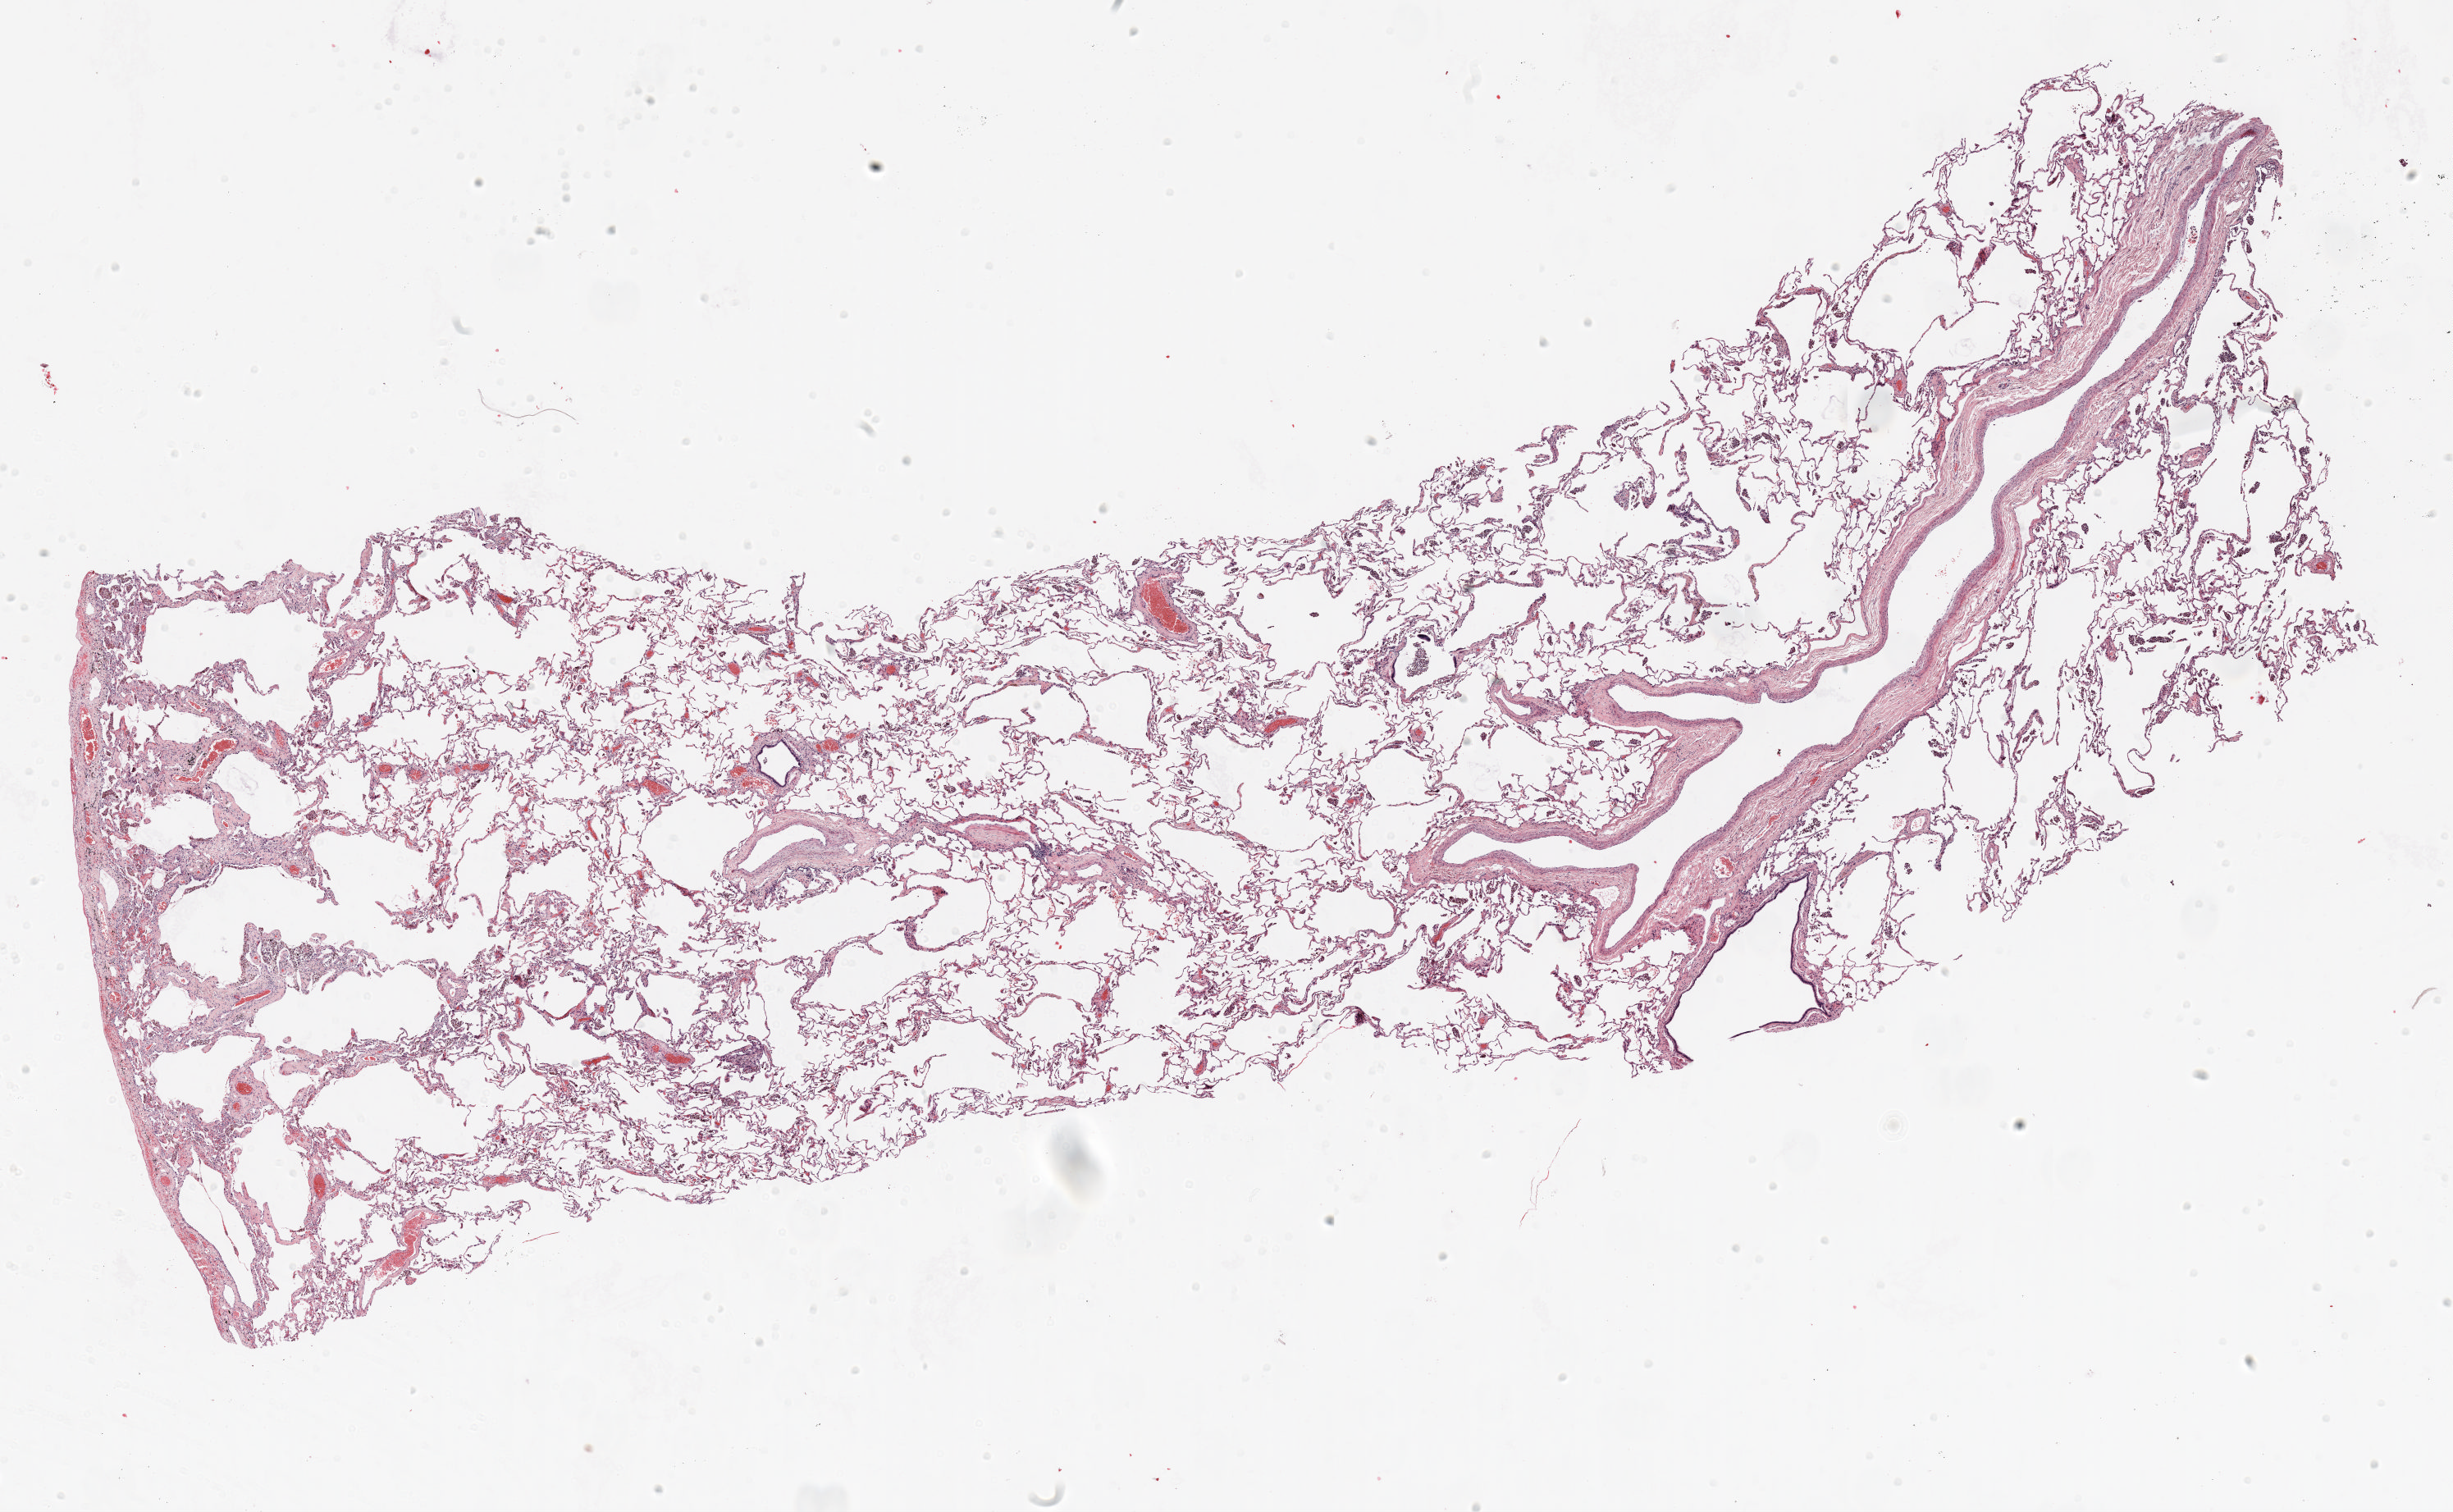
H&E whole-slide image, whole scanned area (about 24.0 x 14.8 mm, from a 20x scan) shown as a low-resolution overview. Formalin-fixed paraffin-embedded (FFPE) section. Lung. Male patient, aged 58 at enrolment. Current smoker at enrolment.
Primary tumour location (clinical record): right upper lobe, right hilum. Participant's lung-cancer diagnosis: Non-small cell carcinoma. Stage (AJCC 6th edition): IB. Tumour size (pathology): 58 mm.